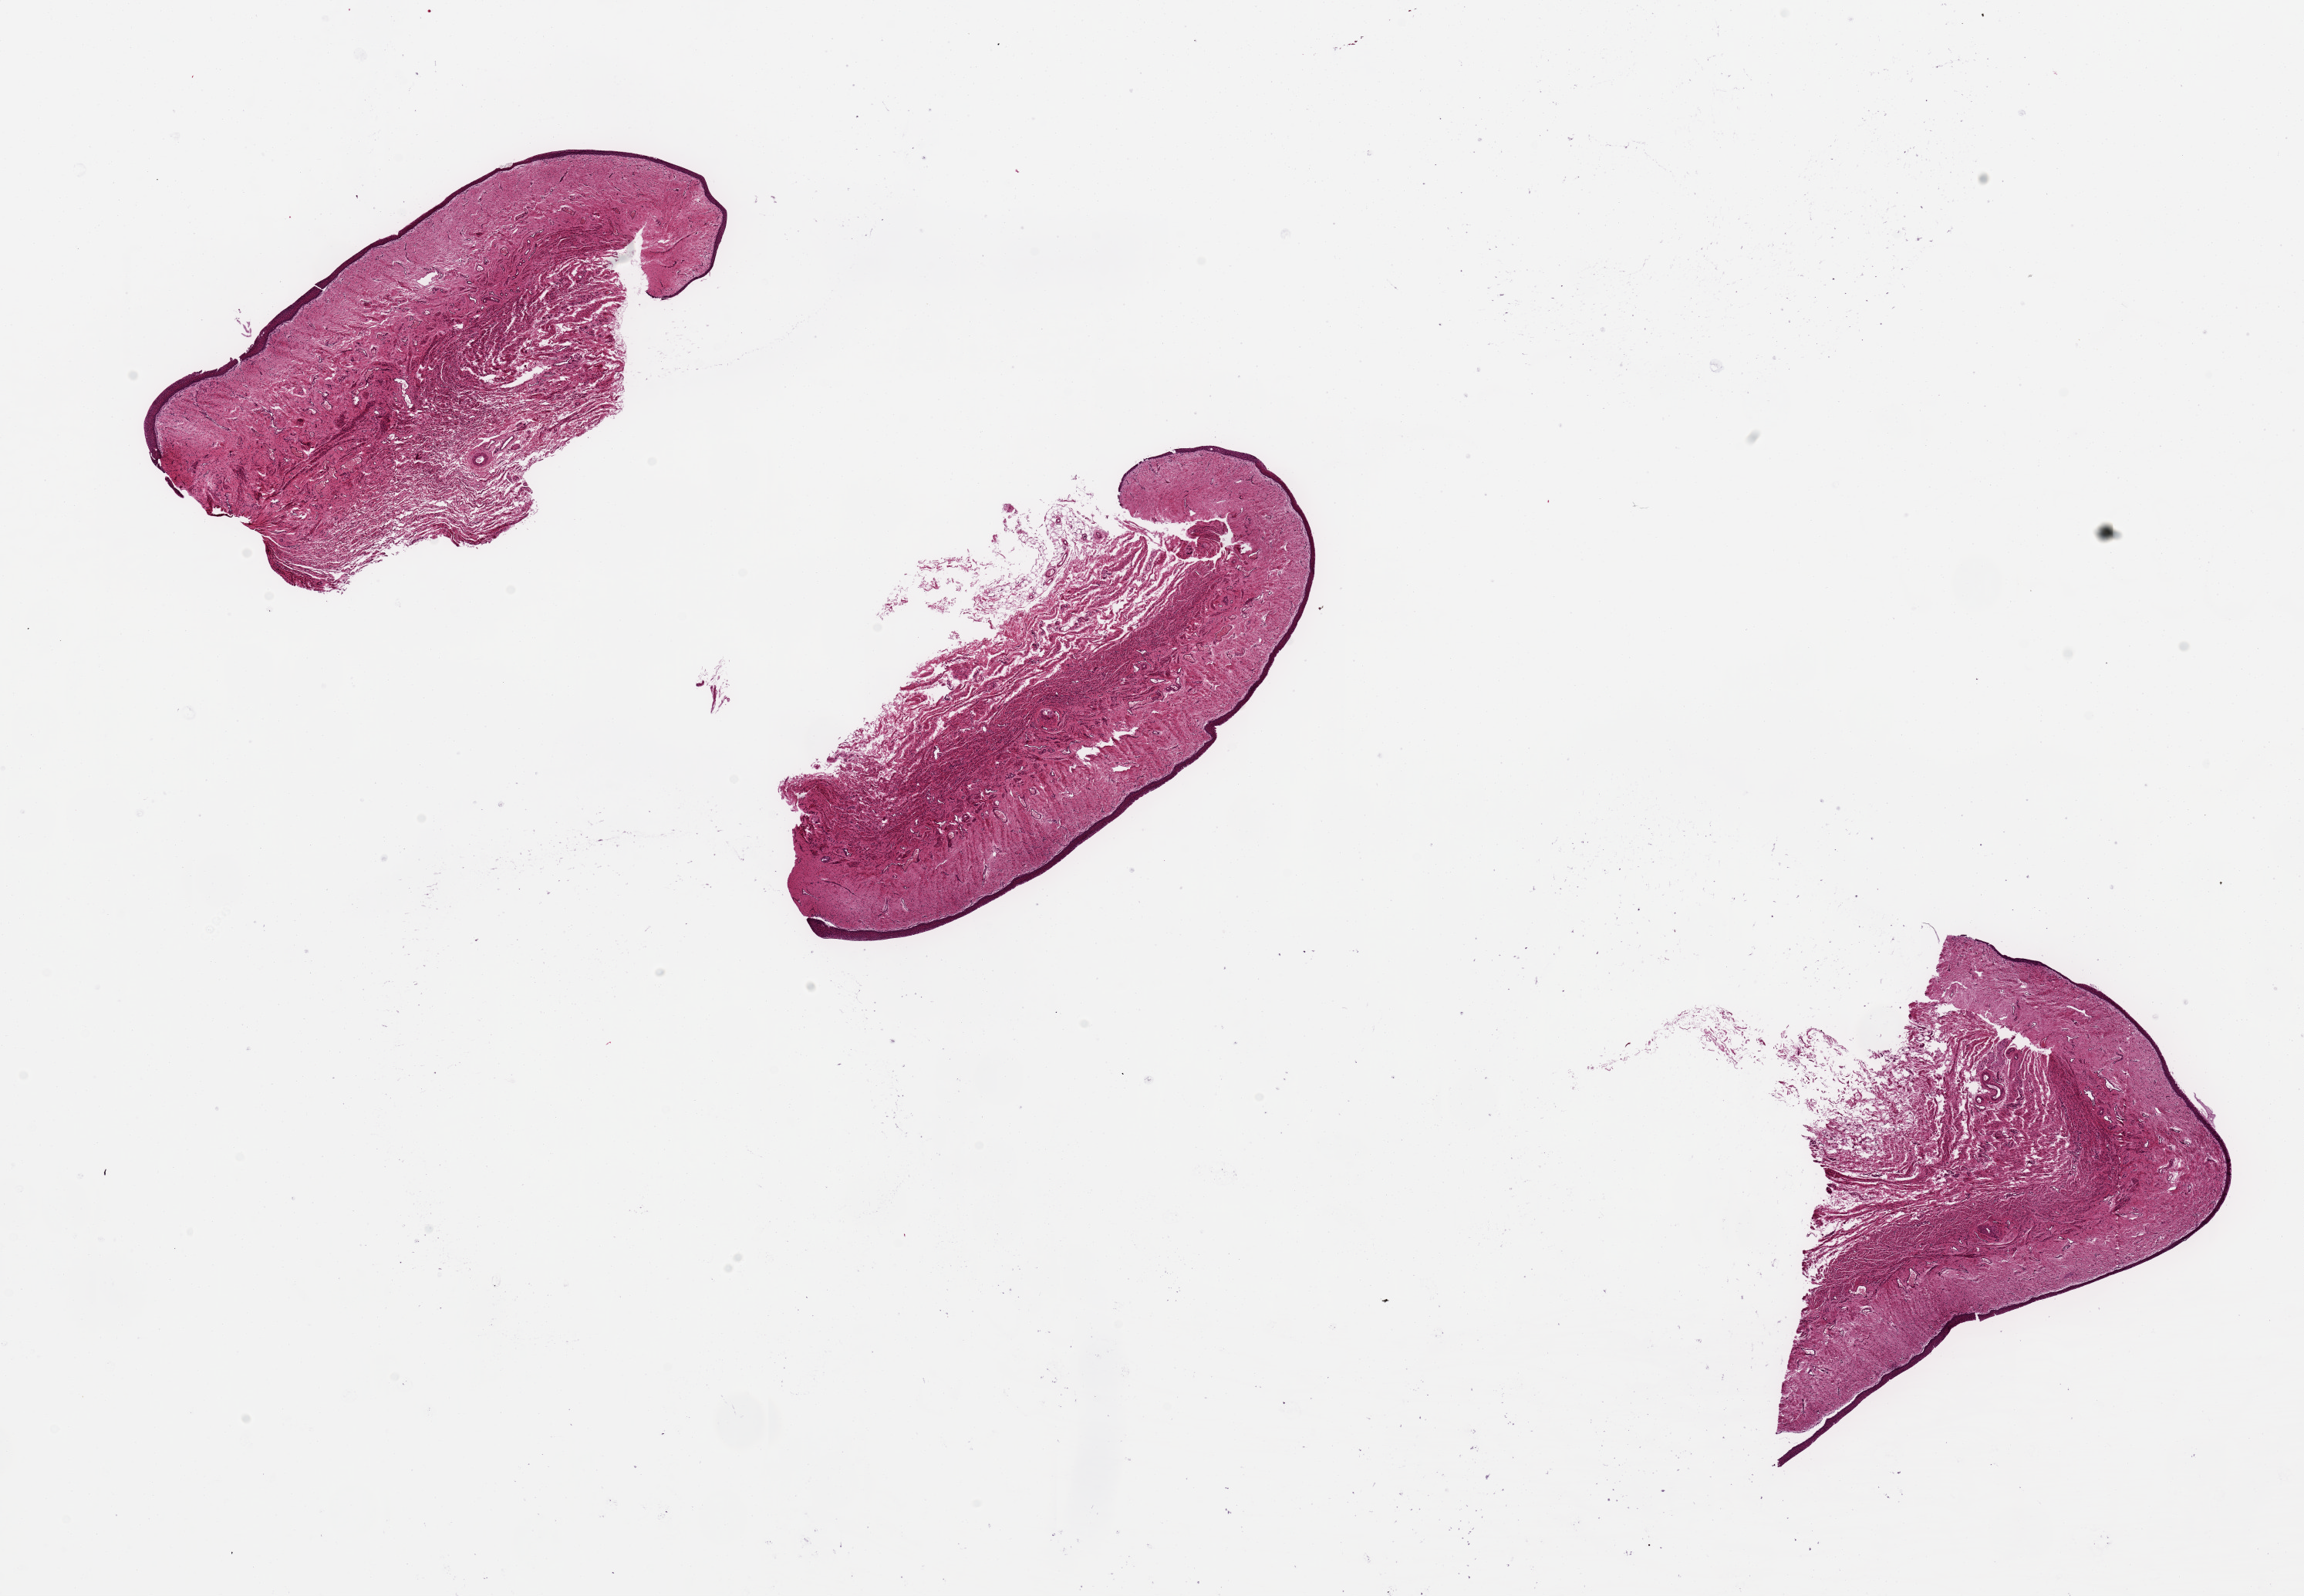
Digitized hematoxylin and eosin (H&E)-stained section, brightfield, shown as a low-resolution overview of the whole scanned area (about 23.6 x 16.4 mm); PAXgene-fixed, paraffin-embedded tissue; sampled site (target tissue): vagina; donor tissue sample. Female donor.
Reviewer comment on this tissue sample: 3 ~6x2.5mm pieces. Non keratinizing squamous mucosa is ~2-3% of specimen thickness.